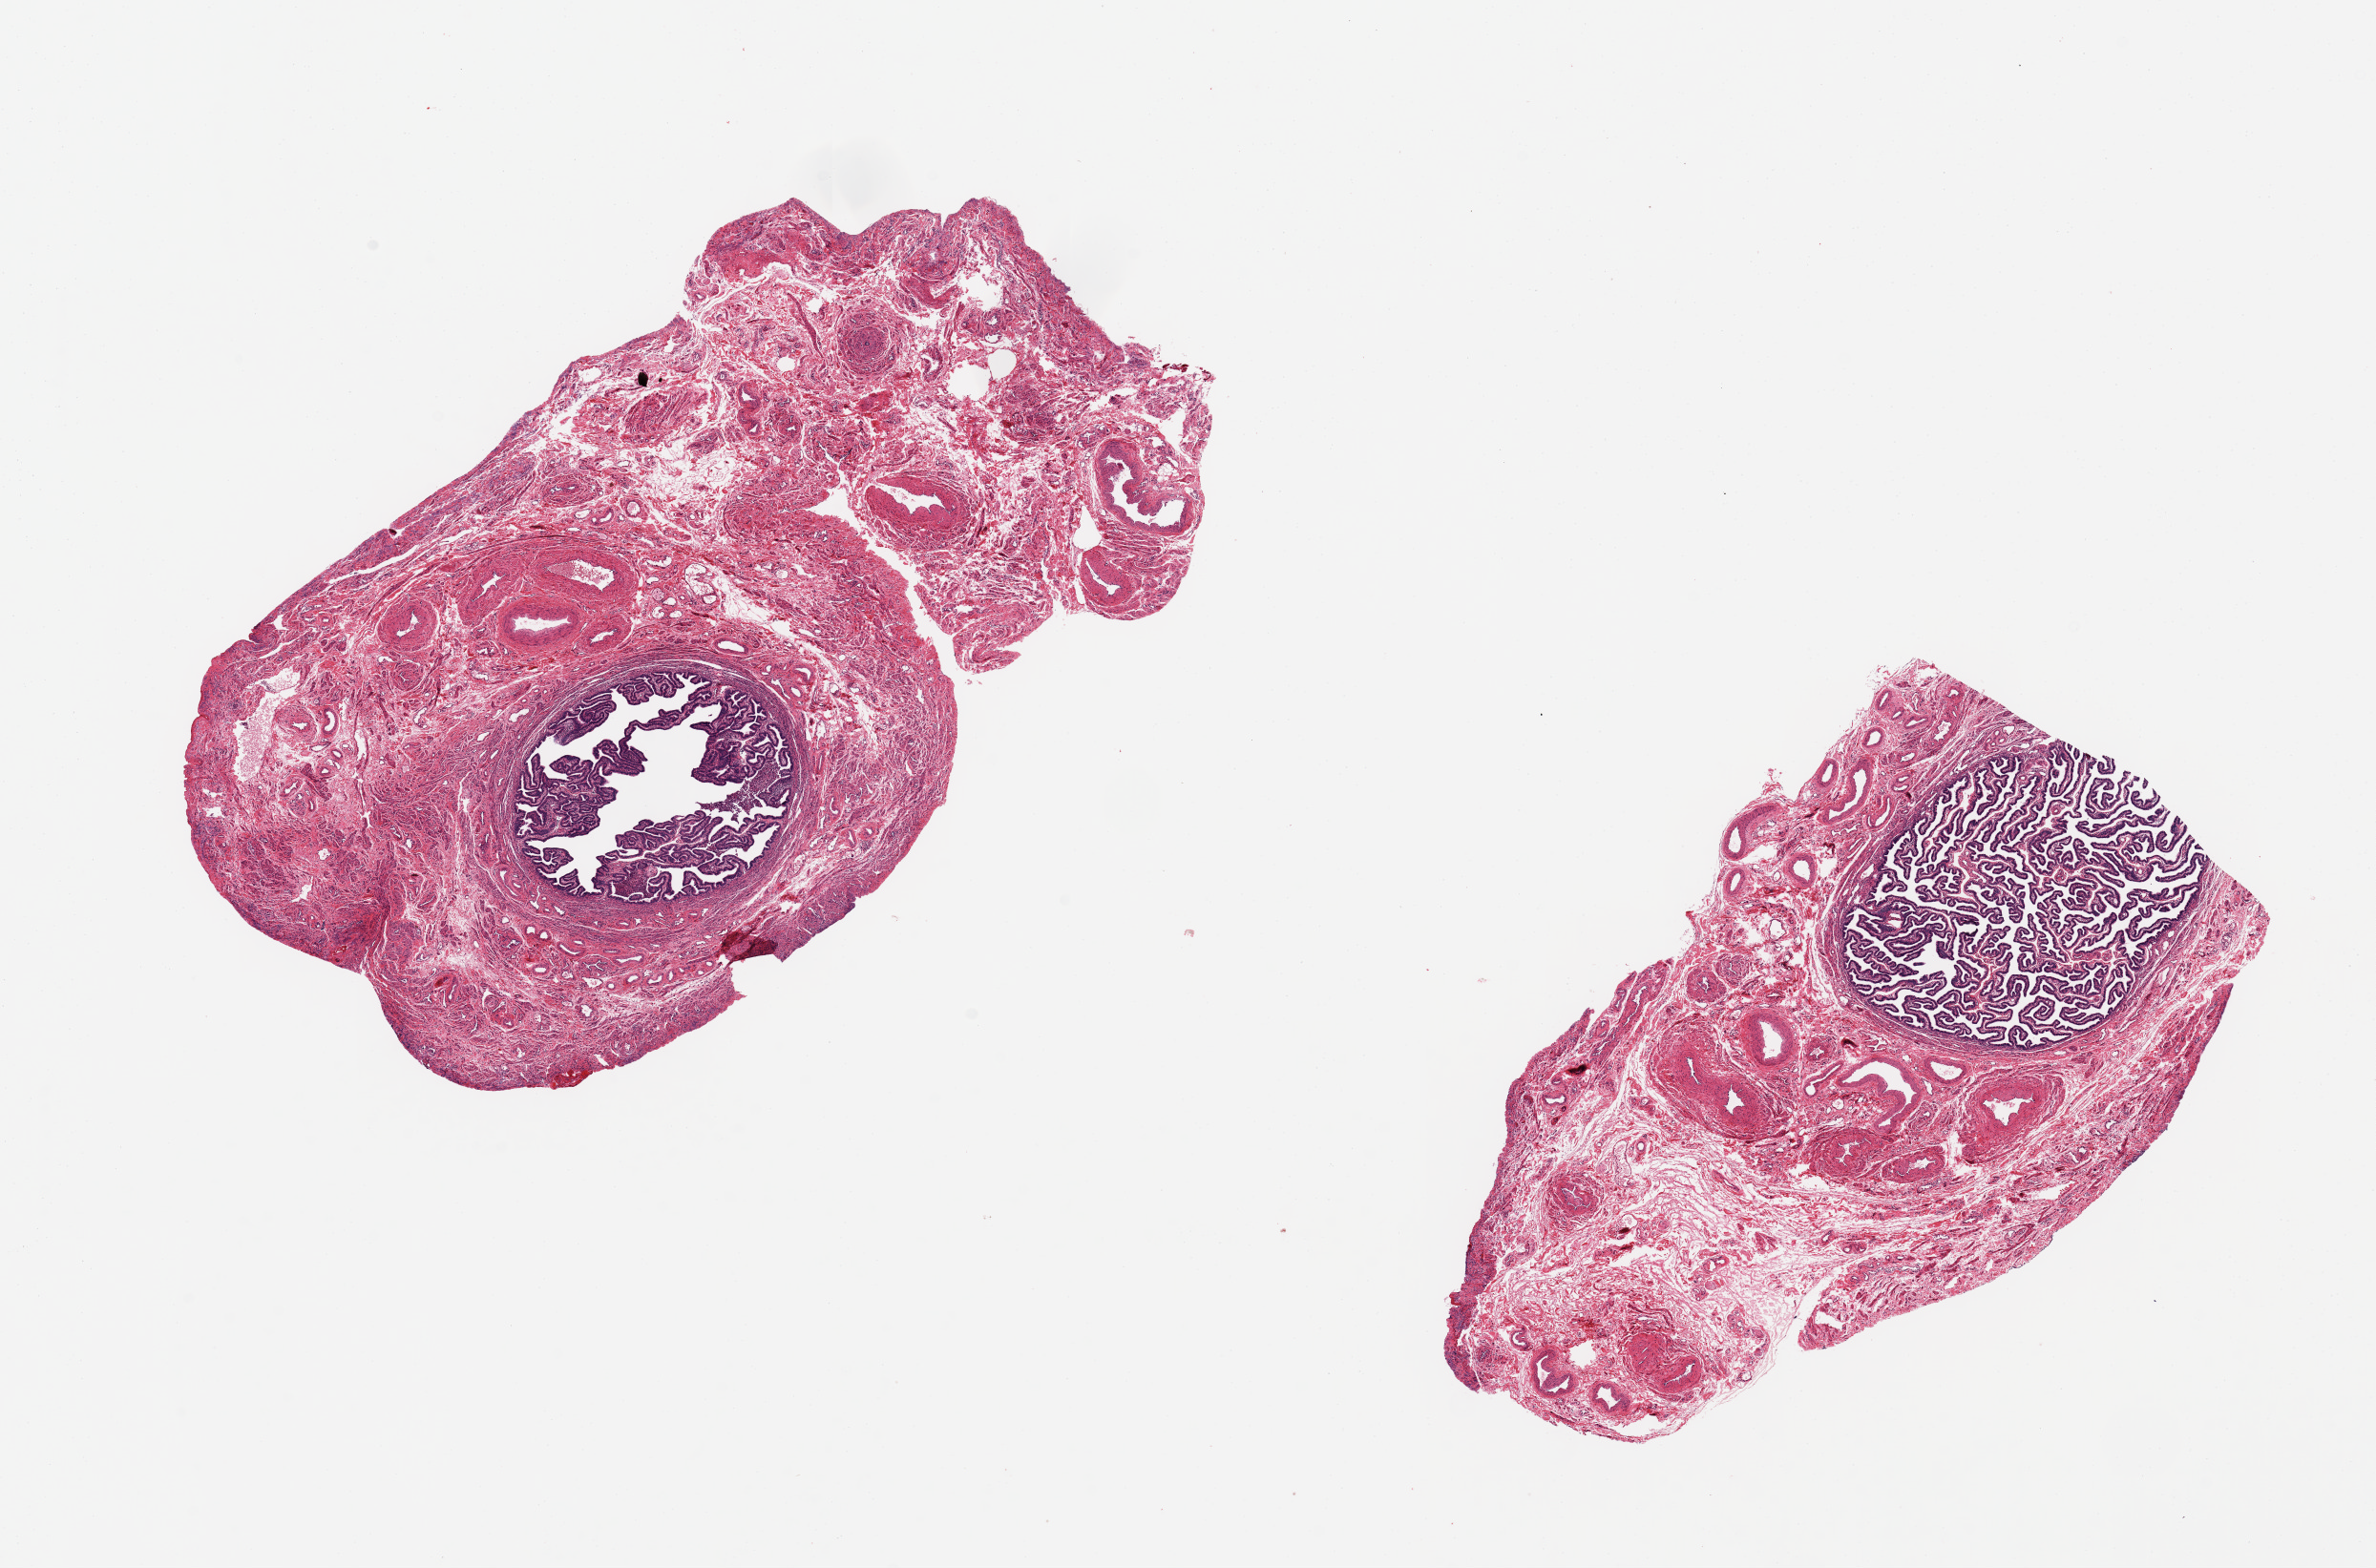
Haematoxylin and eosin whole-slide image — whole scanned area (about 19.7 x 13.0 mm, slide scanned at 20x) shown as a low-resolution overview. PAXgene-fixed, paraffin-embedded tissue. Sampled site (target tissue): fallopian tube. Donor tissue sample. Donor sex: female.
Review note (as recorded): 2 pieces, 9x5 & 7x4 mm; tube comprises ~20-30% of specimens.